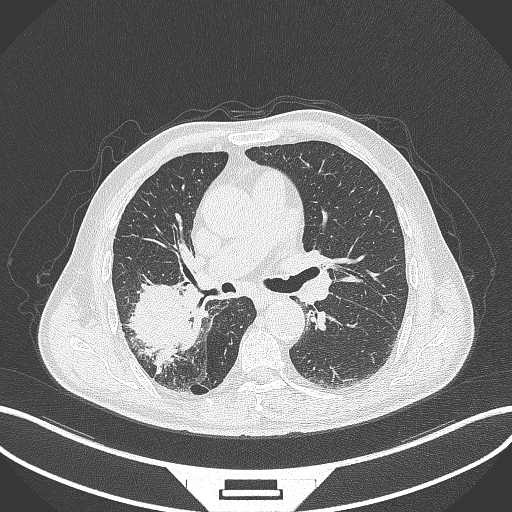
Chest CT, one axial slice; position 237 of 429 along the scan axis; reconstruction kernel B70f; 120 kVp; lung window (W 1500 / L -600 HU); 1 mm slice thickness; 512 × 512 image matrix, field of view 400 × 400 mm. Male patient, age 72 years. Case-level facts recorded for this patient, not image findings: clinical TNM (as recorded): T3 N2 M0.
Structures marked on this image (bounding box drawn by a radiologist):
- lung tumour (recorded histology: adenocarcinoma): box from (x=125, y=274) to (x=197, y=370) px